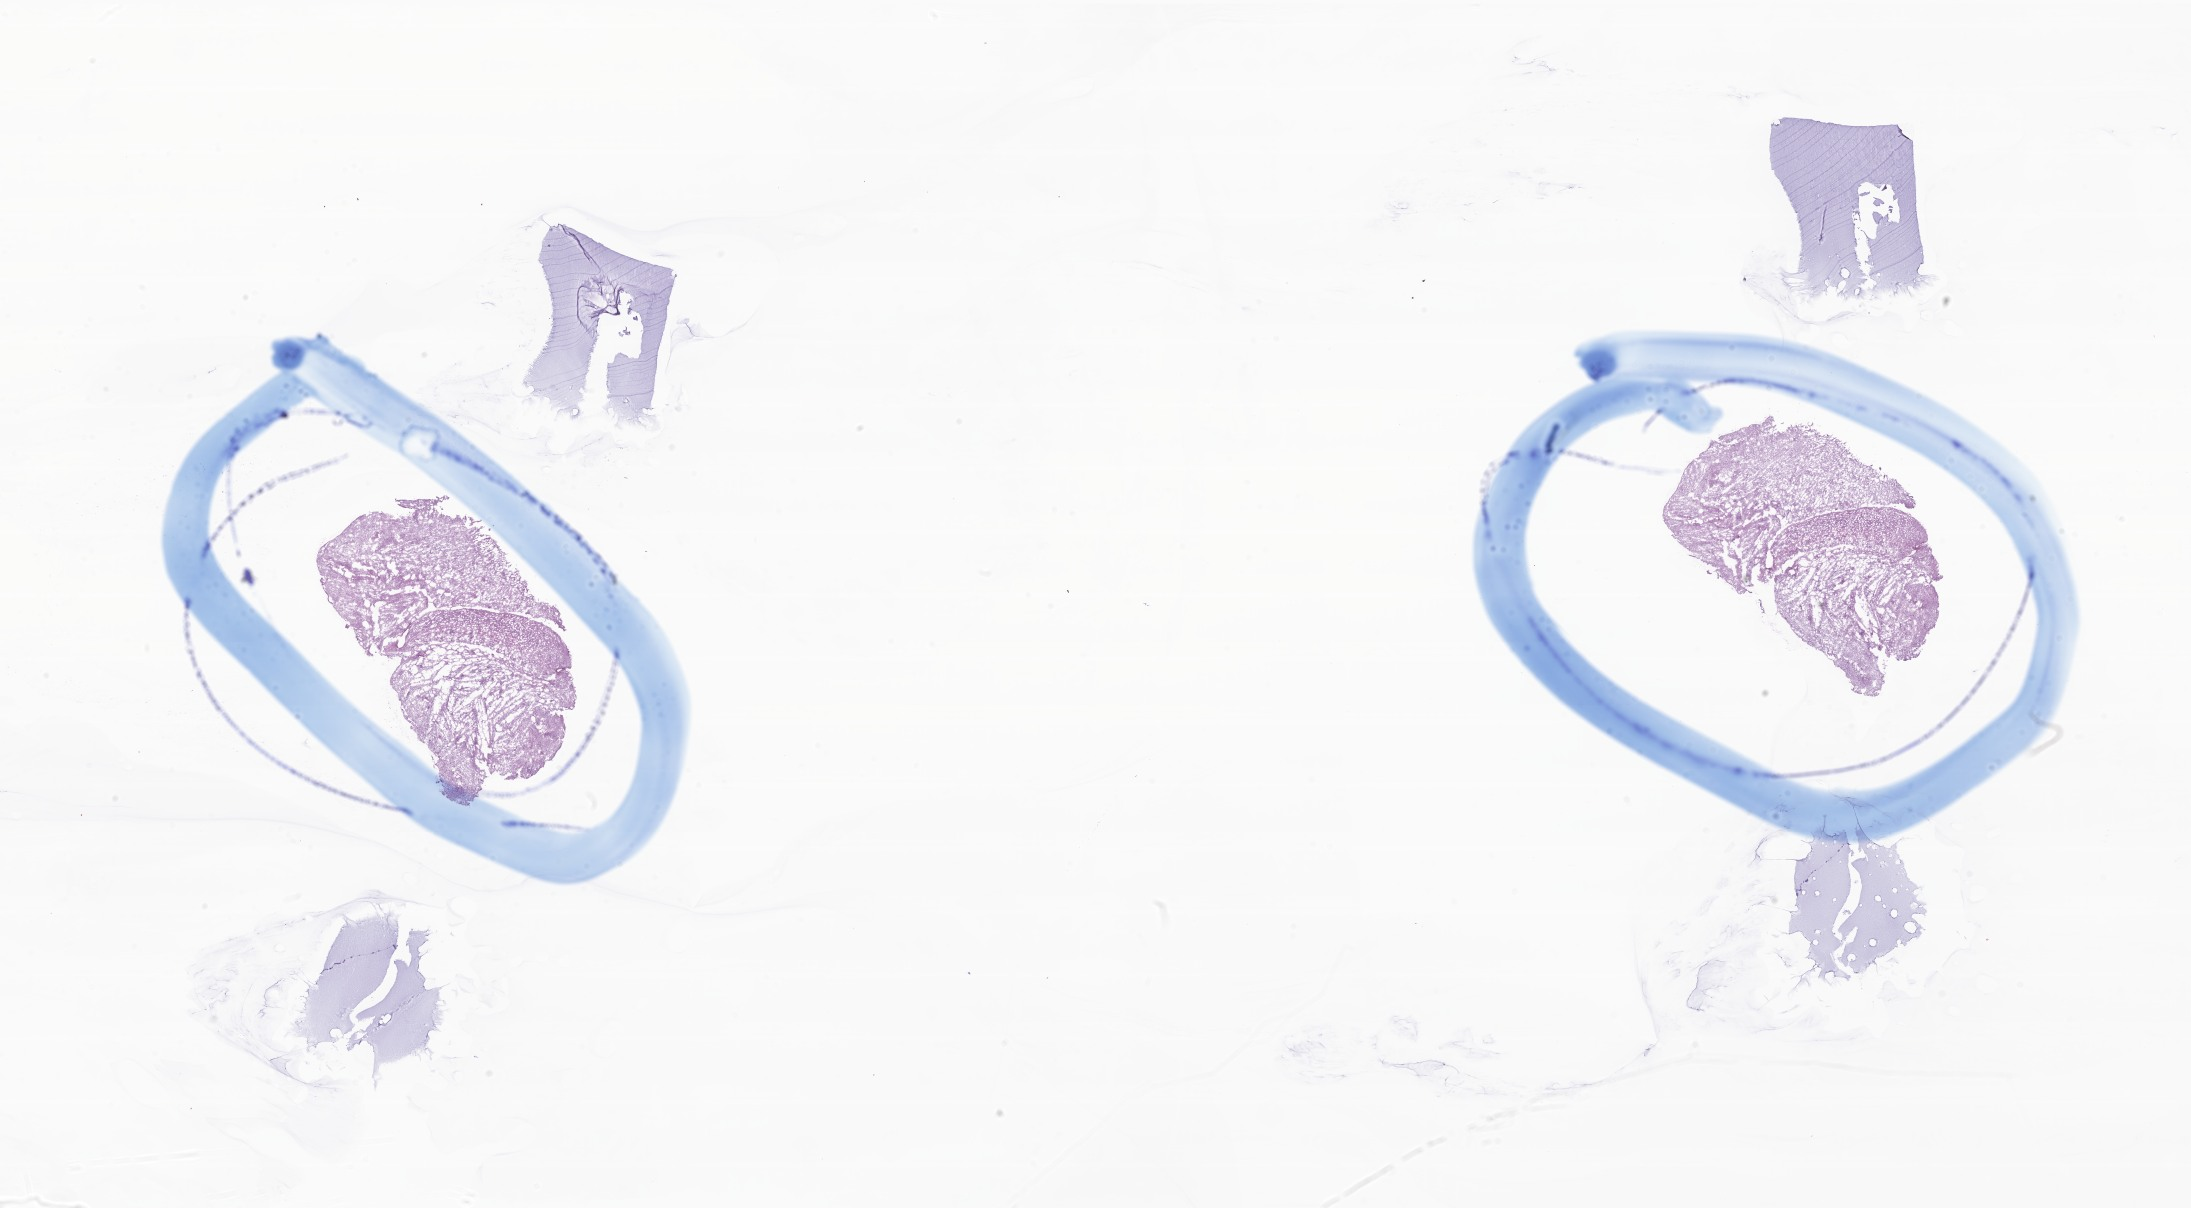
Digitized hematoxylin and eosin (H&E)-stained section of tumor tissue from the brain stem — shown as a low-resolution overview of the whole scanned area (about 36.9 x 20.4 mm); frozen section. Patient: female, age 207 months (17 years 3 months).
Recorded diagnosis: Pilocytic astrocytoma.